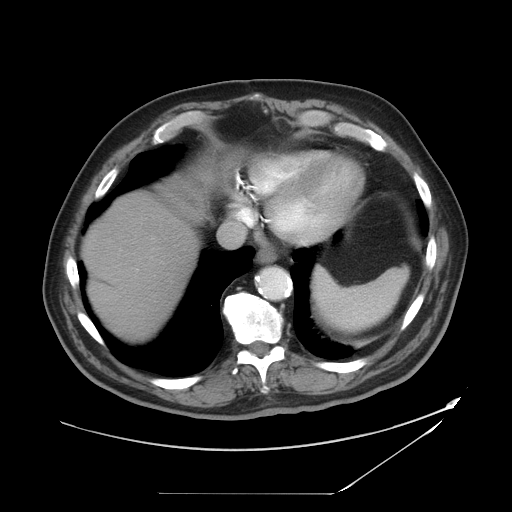
Contrast-enhanced abdominal CT, one axial slice; slice 40 of 49 in the series (ordered by position); reconstruction kernel STANDARD; 120 kVp; intravenous contrast given; soft-tissue window (W 400 / L 40 HU); 5 mm slice thickness; 512 × 512 image matrix, field of view 461 × 461 mm. Male patient, age 72 years. From the clinical record (not read from this slice): diagnosis: colorectal cancer liver metastases, imaged before liver resection; multiple liver metastases: no; largest metastasis: 2.5 cm; disease in both lobes: no.
Annotated regions visible in this slice (outlined manually by an expert reader):
- liver: bounding box (x1, y1, x2, y2) in pixels: (84, 195, 196, 341)
- planned liver remnant (the part of the liver to remain after resection): (85, 195, 196, 341)